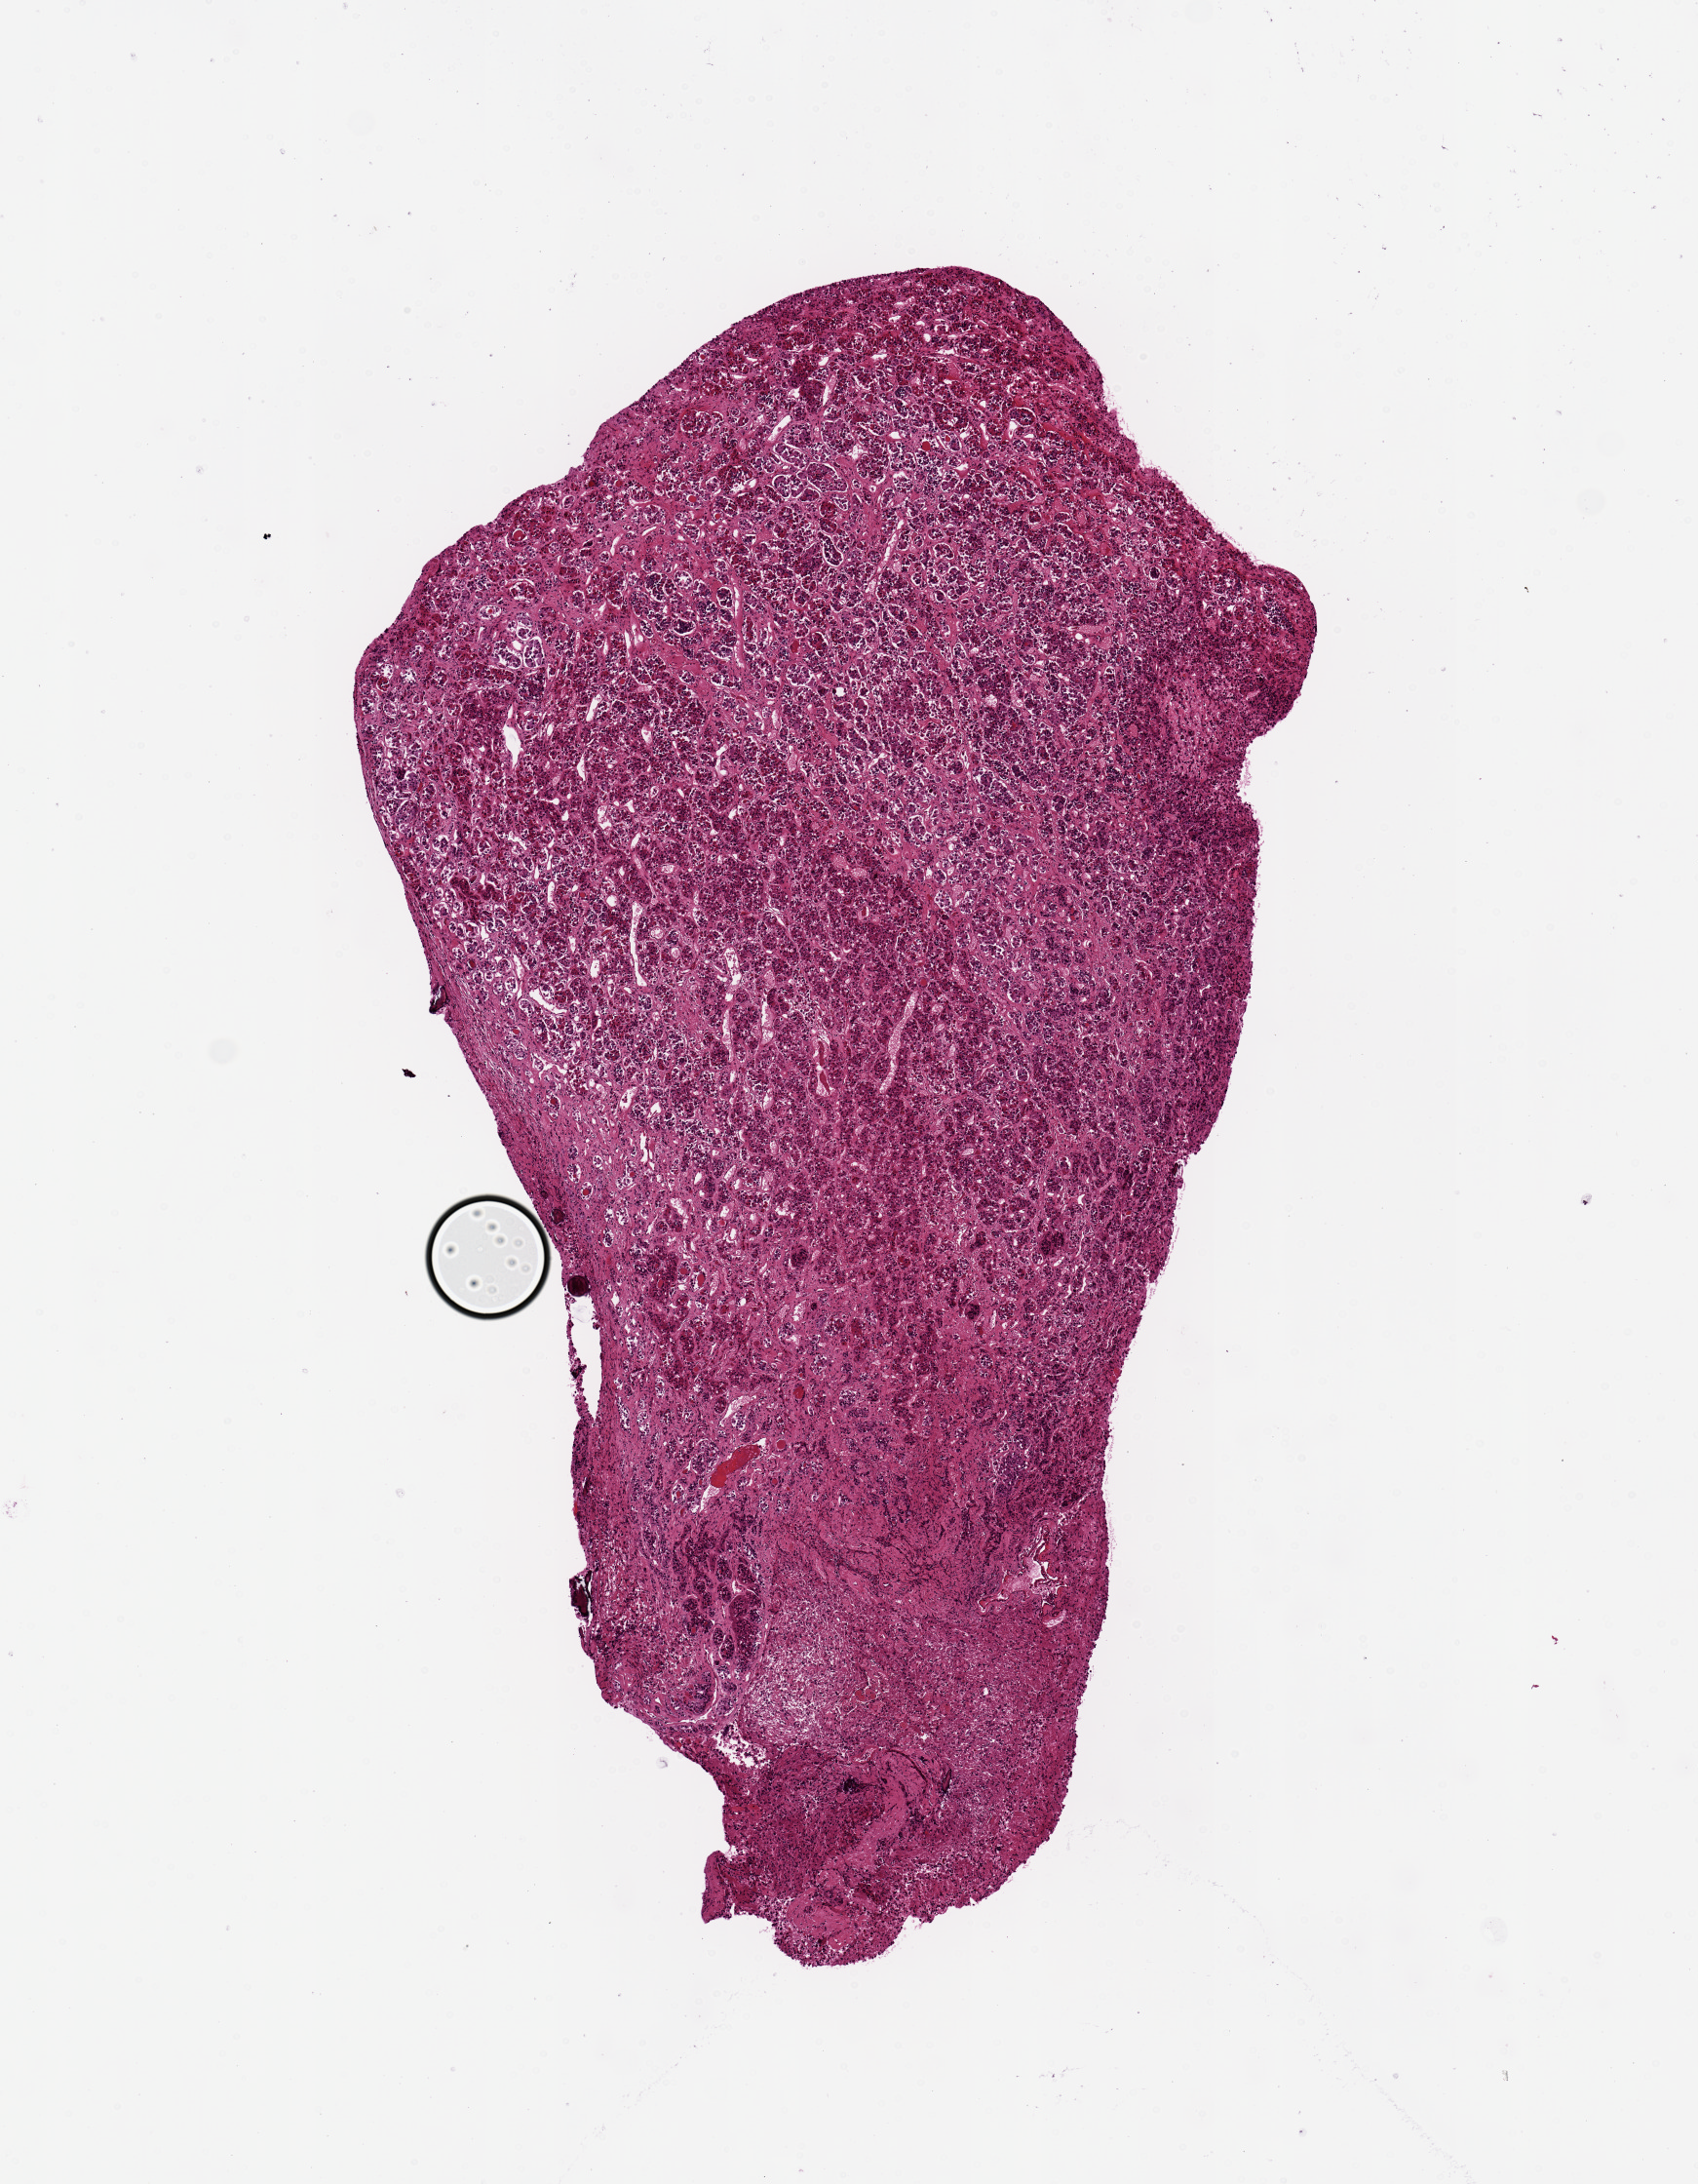
Whole-slide image, hematoxylin and eosin (H&E) stain — shown as a low-resolution overview of the whole scanned area (about 6.9 x 8.9 mm); PAXgene-fixed paraffin-embedded (PFPE) section; section of pituitary (target tissue); tissue donor sample. Male donor.
* pathologist's review note for this sample: Well-preserved